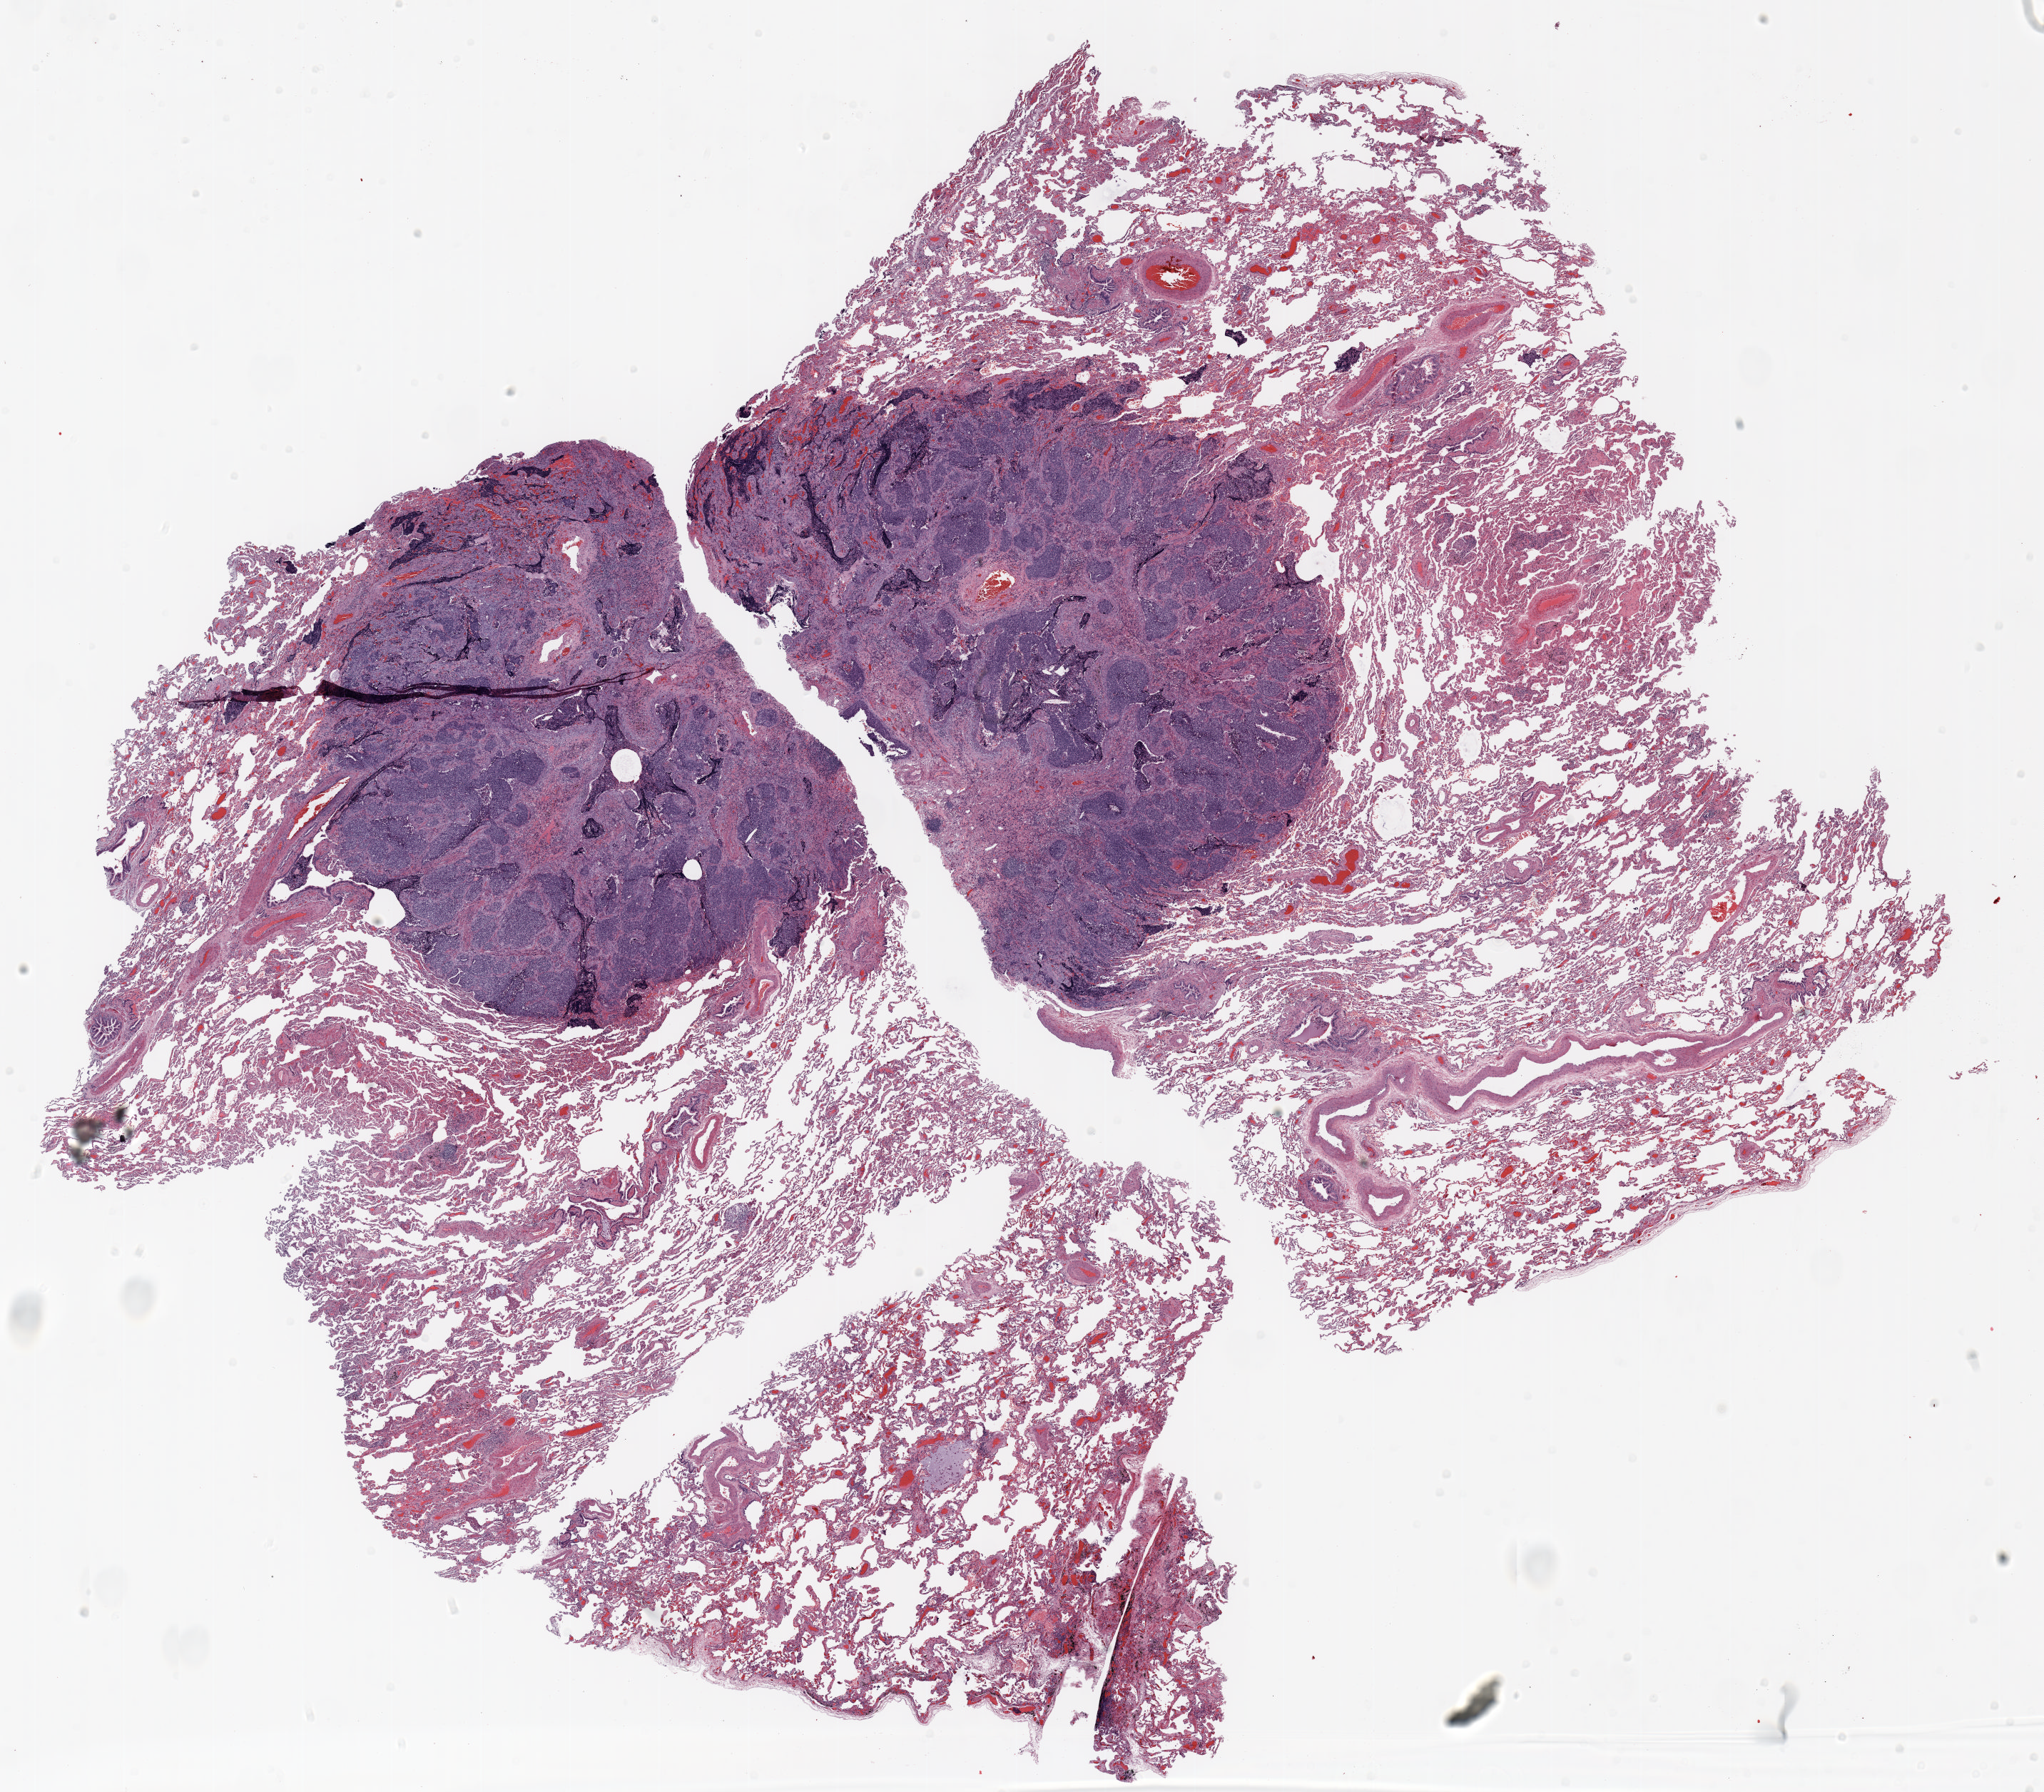
Whole-slide histology image, H&E — low-resolution overview of the scanned area, about 23.0 x 20.2 mm (from a 20x scan), formalin-fixed paraffin-embedded (FFPE) section, lung tissue. Male, age 59 at enrolment. Former smoker at enrolment. Grade: poorly differentiated (G3).
* participant's lung-cancer diagnosis: Large cell carcinoma, NOS
* stage (AJCC 6th edition): IA
* primary tumour location (clinical record): left lower lobe
* tumour size (pathology): 14 mm